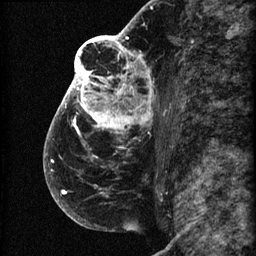
Breast MRI (dynamic contrast-enhanced), one sagittal slice; slice 41 of 60 in the series (ordered by position); 3 images stored at this slice position (order not interpretable as contrast timing); 1.5 T; TE 4.2 ms, TR 22.7 ms; 2 mm slice thickness; 256 × 256 image matrix, field of view 180 × 180 mm. Female patient, age 48 years. From the clinical record (not read from this slice): setting: breast cancer imaged before/during neoadjuvant chemotherapy; receptor status: triple-negative.
Outlined on this slice (semi-automatic segmentation, software-assisted and operator-edited):
- analysis volume of interest (the breast-tissue region the enhancement analysis was run in; not a lesion): bounding box (x1, y1, x2, y2) in pixels: (44, 30, 173, 207)
- tumour enhancement mask (voxels above the 90 % enhancement threshold inside the analysis volume of interest): (44, 30, 153, 194)